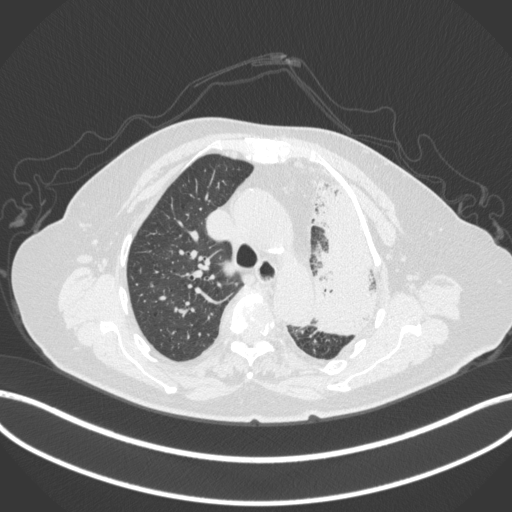
Chest CT, one axial slice. Position 286 of 399 along the scan axis. Lung window (W 1500 / L -600 HU). 1 mm slice thickness. 512 × 512 image matrix, field of view 400 × 400 mm. Female patient, age 75 years. From the clinical record (not read from this slice): clinical TNM (as recorded): T3 N3 M1.
Structures marked on this image (bounding box drawn by a radiologist):
- lung tumour (recorded histology: adenocarcinoma): bounding box [x1, y1, x2, y2] px = [308, 180, 387, 335]